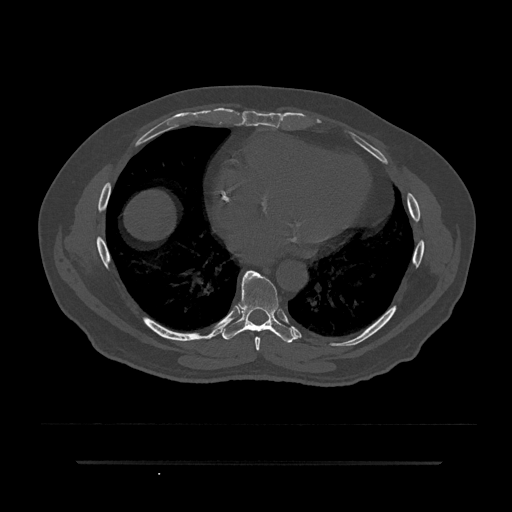
CT including the spine, one axial slice; slice 441 of 797 in the series (ordered by position); reconstruction kernel Br40s/3; 120 kVp; bone window (W 1800 / L 400 HU); 0.5 mm slice thickness; 512 × 512 image matrix. Male patient, age 59 years. Case-level facts recorded for this patient, not image findings: primary cancer: bile ducts; vertebrae with lytic lesions (as recorded): T10.
Outlined on this slice (semi-automatically segmented with operator editing):
- T7 vertebra: bounding box <245,273,261,351> (left, top, right, bottom; pixels)
- T8 vertebra: <222,271,295,343>